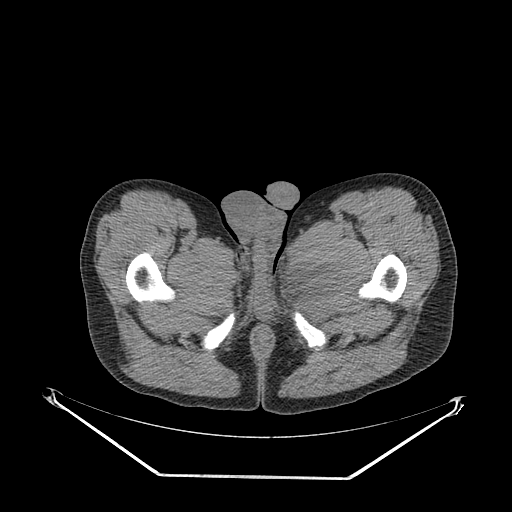
CT of an extremity soft-tissue mass (from a PET/CT study), one axial slice. Slice 43 of 267 in the series (ordered by position). Reconstruction kernel SOFT. Soft-tissue window (W 400 / L 40 HU). 3.75 mm slice thickness. 512 × 512 image matrix, field of view 500 × 500 mm. Male patient. From the clinical record (not read from this slice): histological type: pleiomorphic liposarcoma; grade: high; site of the primary tumour: left thigh.
Annotated regions visible in this slice (expert contour drawn on MRI and transferred to this co-registered scan by the dataset authors):
- gross tumour volume including surrounding oedema: bounding box (x1, y1, x2, y2) in pixels: (288, 260, 346, 318)
- gross tumour volume (mass): (297, 265, 334, 295)